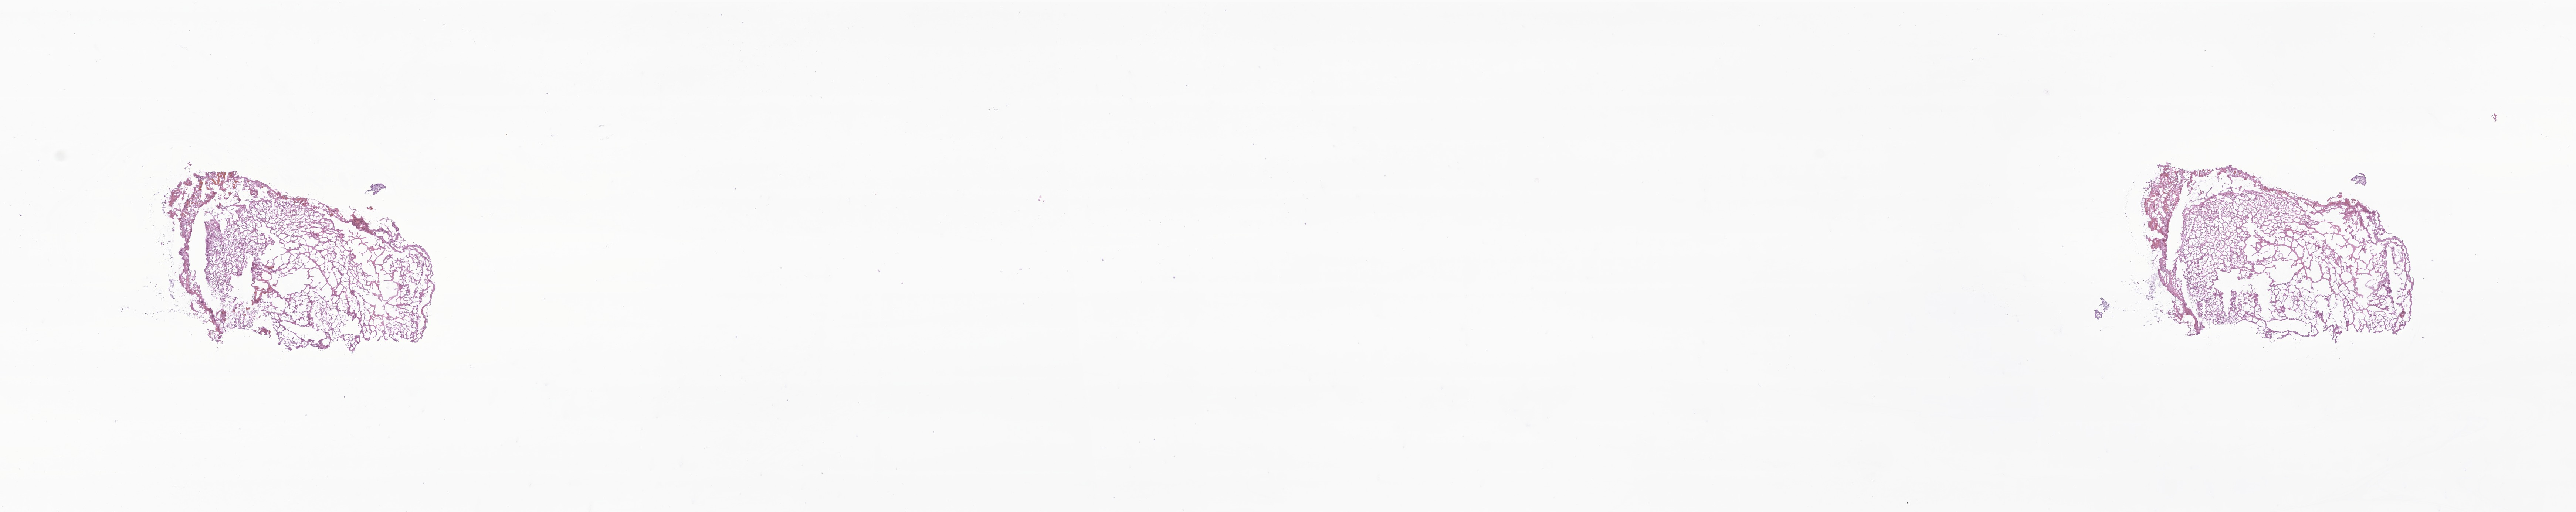
Whole-slide image, haematoxylin and eosin stain of tumor tissue from the cerebellum, whole scanned area (about 29.4 x 5.8 mm) shown as a low-resolution overview. Frozen section (OCT-embedded). Patient: male, age 108 months (9 years).
Diagnosis (ICD-O-3 morphology term): Pilocytic astrocytoma.